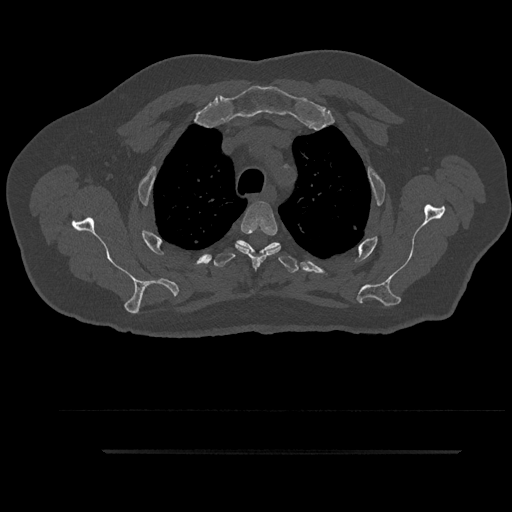
CT including the spine, one axial slice; position 703 of 797 along the scan axis; 120 kVp; bone window (W 1800 / L 400 HU); 512 × 512 image matrix, field of view 432 × 432 mm. Male patient, age 63 years. From the clinical record (not read from this slice): primary cancer: renal.
Annotated regions visible in this slice (semi-automatically segmented with operator editing):
- T3 vertebra: bounding box (x1, y1, x2, y2) in pixels: (235, 201, 281, 268)
- T4 vertebra: (211, 240, 299, 273)